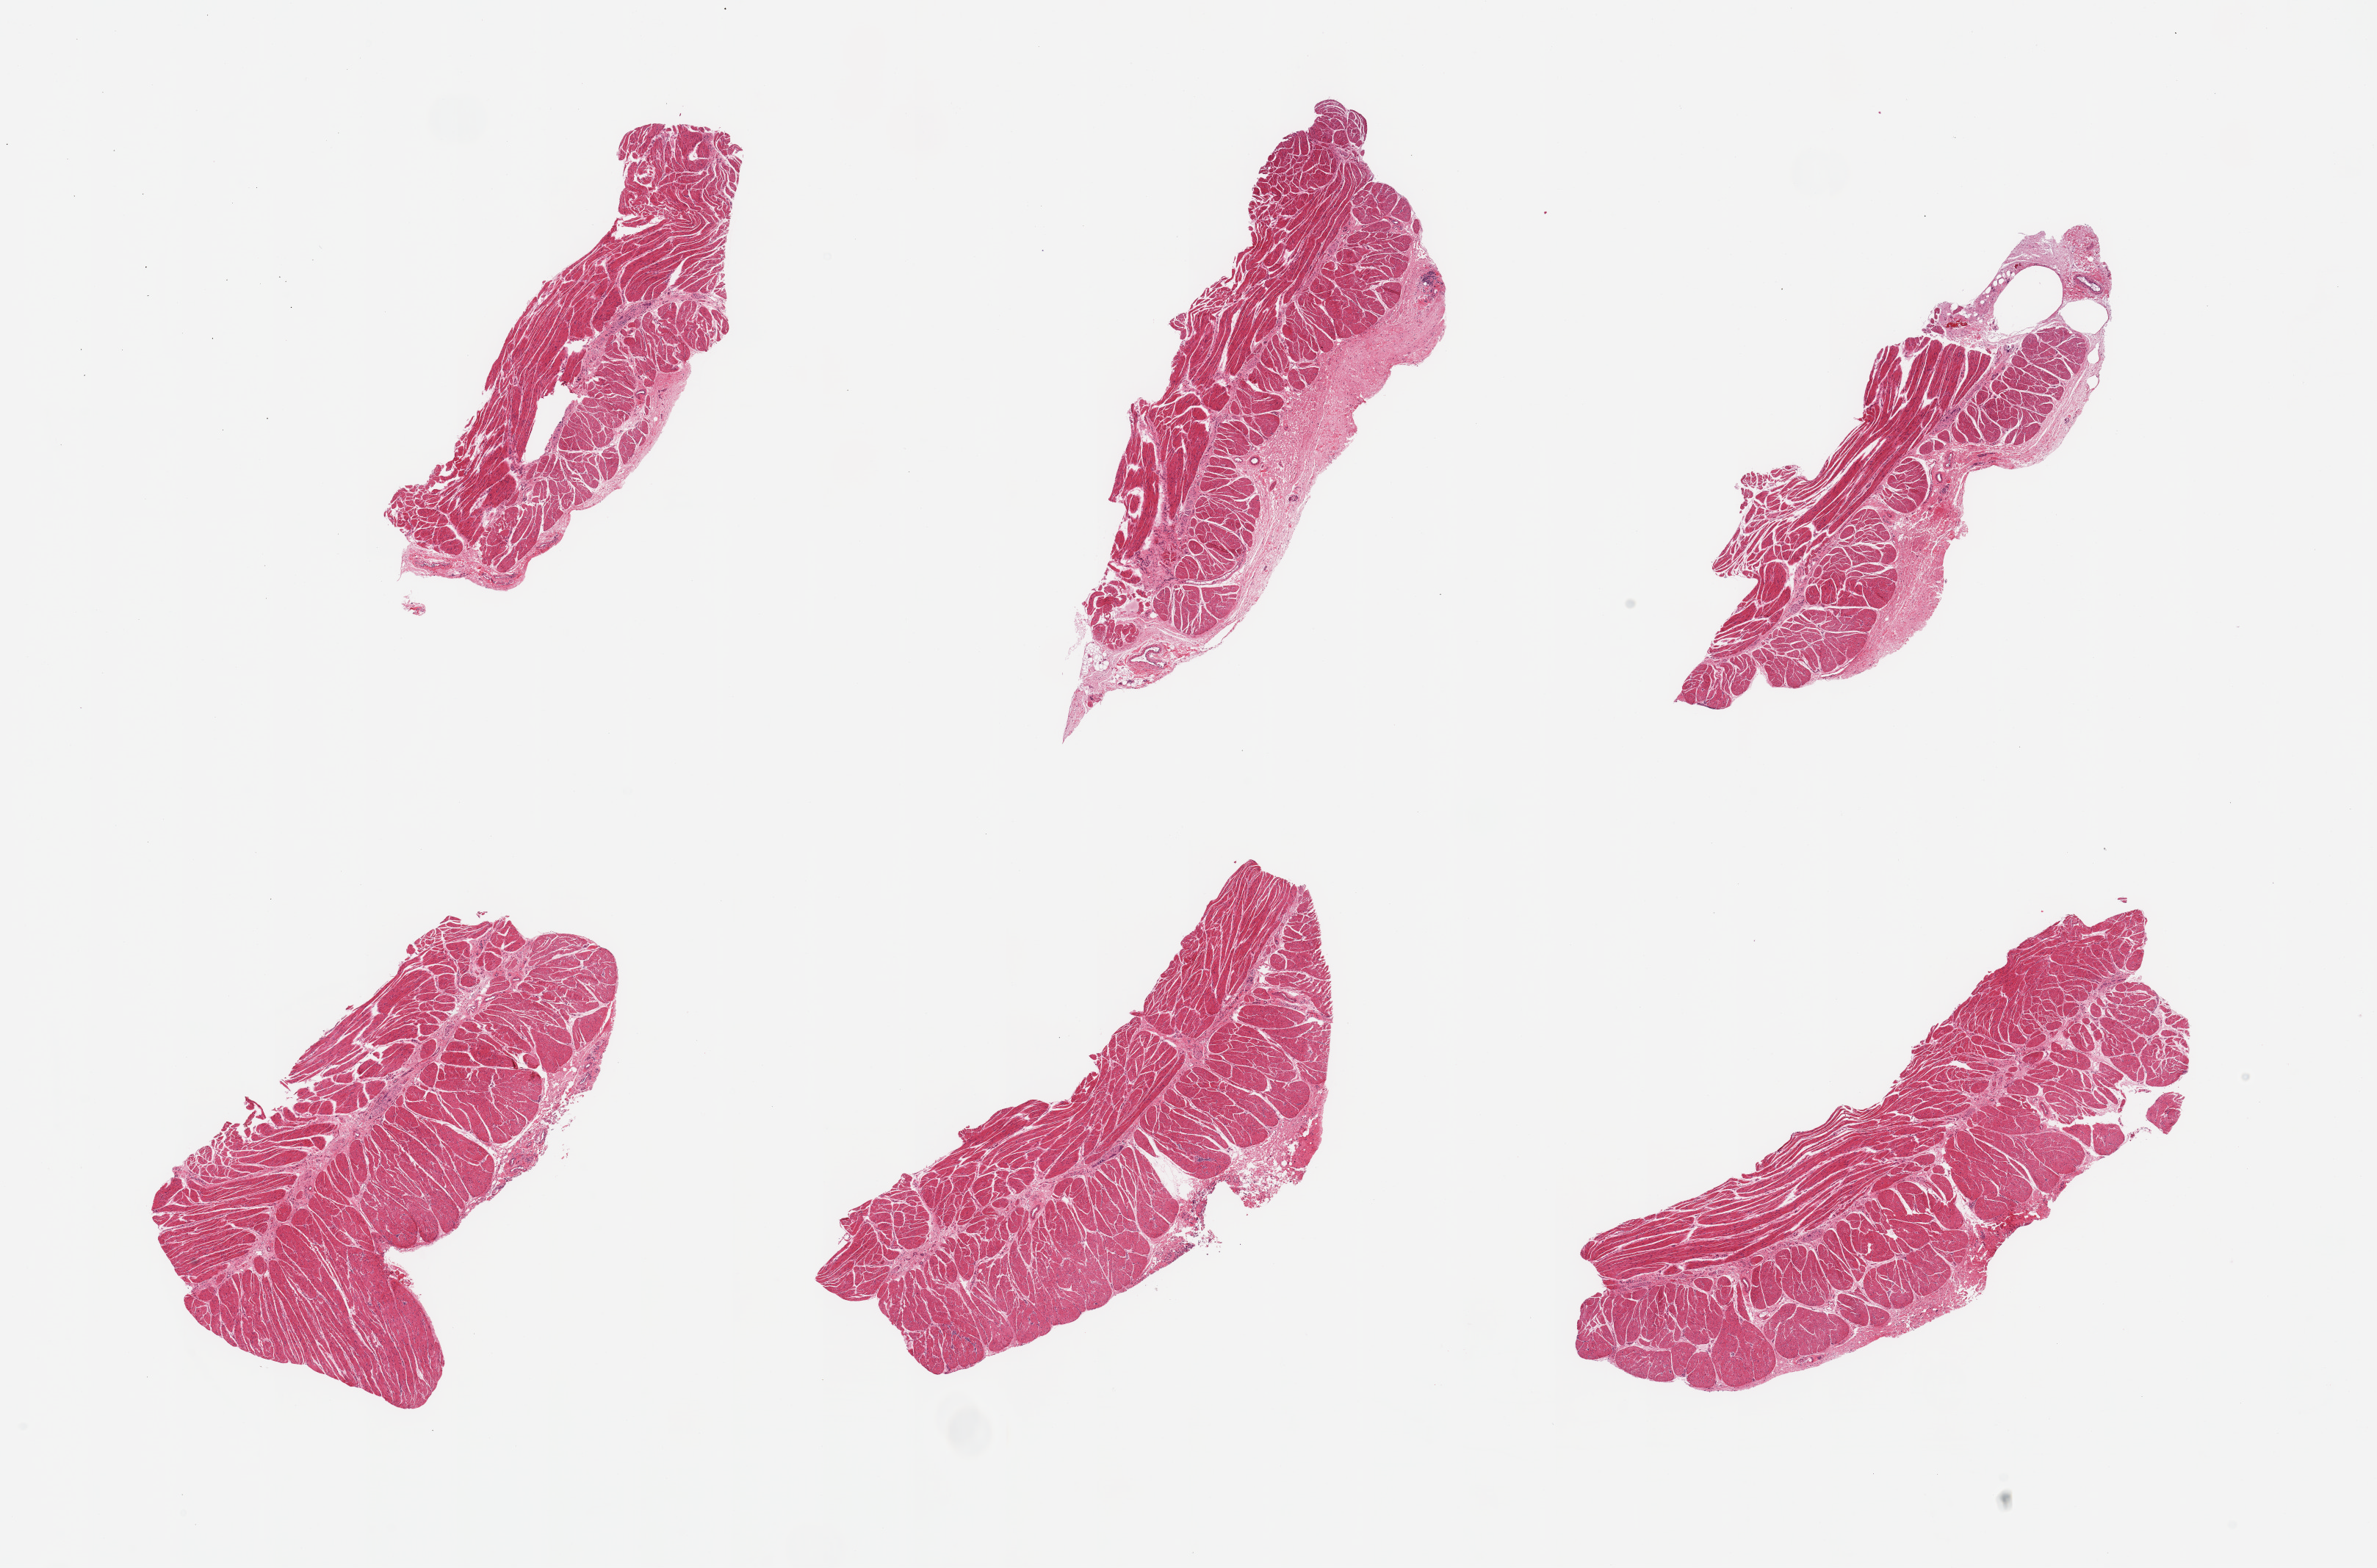
H&E whole-slide image — shown as a low-resolution overview of the whole scanned area (about 25.6 x 16.9 mm), PAXgene-fixed paraffin-embedded (PFPE) section, sampled site (target tissue): esophageal muscle, donor tissue sample. Donor: female.
• pathologist's review note for this sample: 6 pieces; well trimmed muscle except for 20% fibrous submucosa on 2 pieces